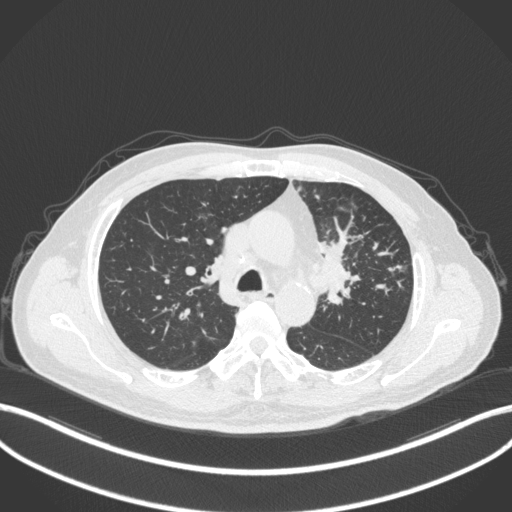
Chest CT, one axial slice; position 236 of 386 along the scan axis; reconstruction kernel B31f; 120 kVp; lung window (W 1500 / L -600 HU); 1 mm slice thickness; 512 × 512 image matrix, field of view 400 × 400 mm. Male patient, age 69 years. Case-level facts recorded for this patient, not image findings: clinical TNM (as recorded): T2a N2 M0.
Outlined on this slice (bounding box drawn by a radiologist):
- lung tumour (recorded histology: adenocarcinoma): box from (x=321, y=232) to (x=356, y=308) px